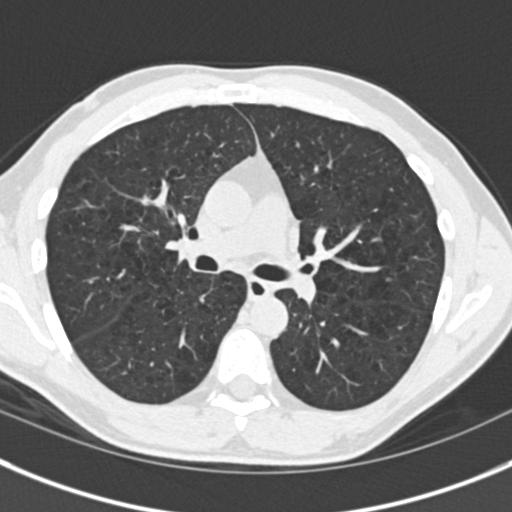
Low-dose screening chest CT, one axial slice. Slice 101 of 175 in the series (ordered by position). Reconstruction kernel B30f. Lung window (W 1500 / L -600 HU). 2 mm slice thickness. 512 × 512 image matrix.
Outlined on this slice (outlined manually by an expert reader):
- lesion 1 (tumor, upper lobe of right lung): box from (x=139, y=195) to (x=151, y=206) px